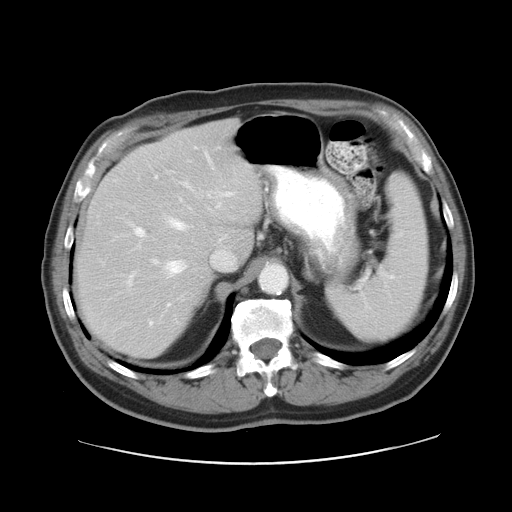
Contrast-enhanced abdominal CT, one axial slice. Slice 20 of 28 in the series (ordered by position). Reconstruction kernel STANDARD. 120 kVp. Intravenous contrast given. Soft-tissue window (W 400 / L 40 HU). 512 × 512 image matrix, field of view 402 × 402 mm. Male patient, age 74 years. Case-level facts recorded for this patient, not image findings: diagnosis: colorectal cancer liver metastases, imaged before liver resection; multiple liver metastases: no; largest metastasis: 5 cm.
Annotated regions visible in this slice (outlined manually by an expert reader):
- hepatic veins: bounding box [x1, y1, x2, y2] px = [127, 153, 221, 286]
- liver: [79, 123, 259, 356]
- planned liver remnant (the part of the liver to remain after resection): [79, 175, 213, 356]
- portal vein (with intrahepatic branches): [135, 146, 230, 237]